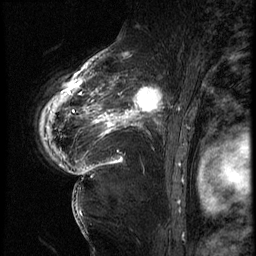
Breast MRI (dynamic contrast-enhanced), one sagittal slice. Slice 46 of 62 in the series (ordered by position). 3 images stored at this slice position (order not interpretable as contrast timing). 1.5 T. TE 4.2 ms, TR 9 ms. 256 × 256 image matrix, field of view 180 × 180 mm. Female patient, age 56 years. Case-level facts recorded for this patient, not image findings: setting: breast cancer imaged before/during neoadjuvant chemotherapy; receptor status: HER2-positive.
Outlined on this slice (semi-automatic segmentation, software-assisted and operator-edited):
- analysis volume of interest (the breast-tissue region the enhancement analysis was run in; not a lesion): bounding box <84,75,181,153> (left, top, right, bottom; pixels)
- tumour enhancement mask (voxels above the 140 % enhancement threshold inside the analysis volume of interest): <84,75,165,135>